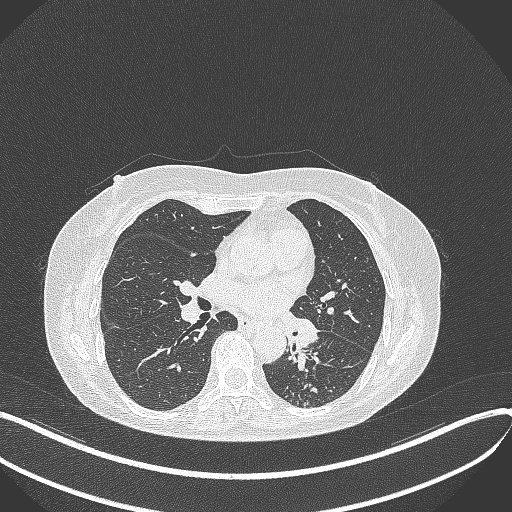
Chest CT, one axial slice; slice 213 of 429 in the series (ordered by position); lung window (W 1500 / L -600 HU); 512 × 512 image matrix, field of view 400 × 400 mm. Patient: female, 63 years. From the clinical record (not read from this slice): clinical TNM (as recorded): T1b N0 M0.
Annotated regions visible in this slice (bounding box drawn by a radiologist):
- lung tumour (recorded histology: adenocarcinoma): bounding box <285,315,324,353> (left, top, right, bottom; pixels)